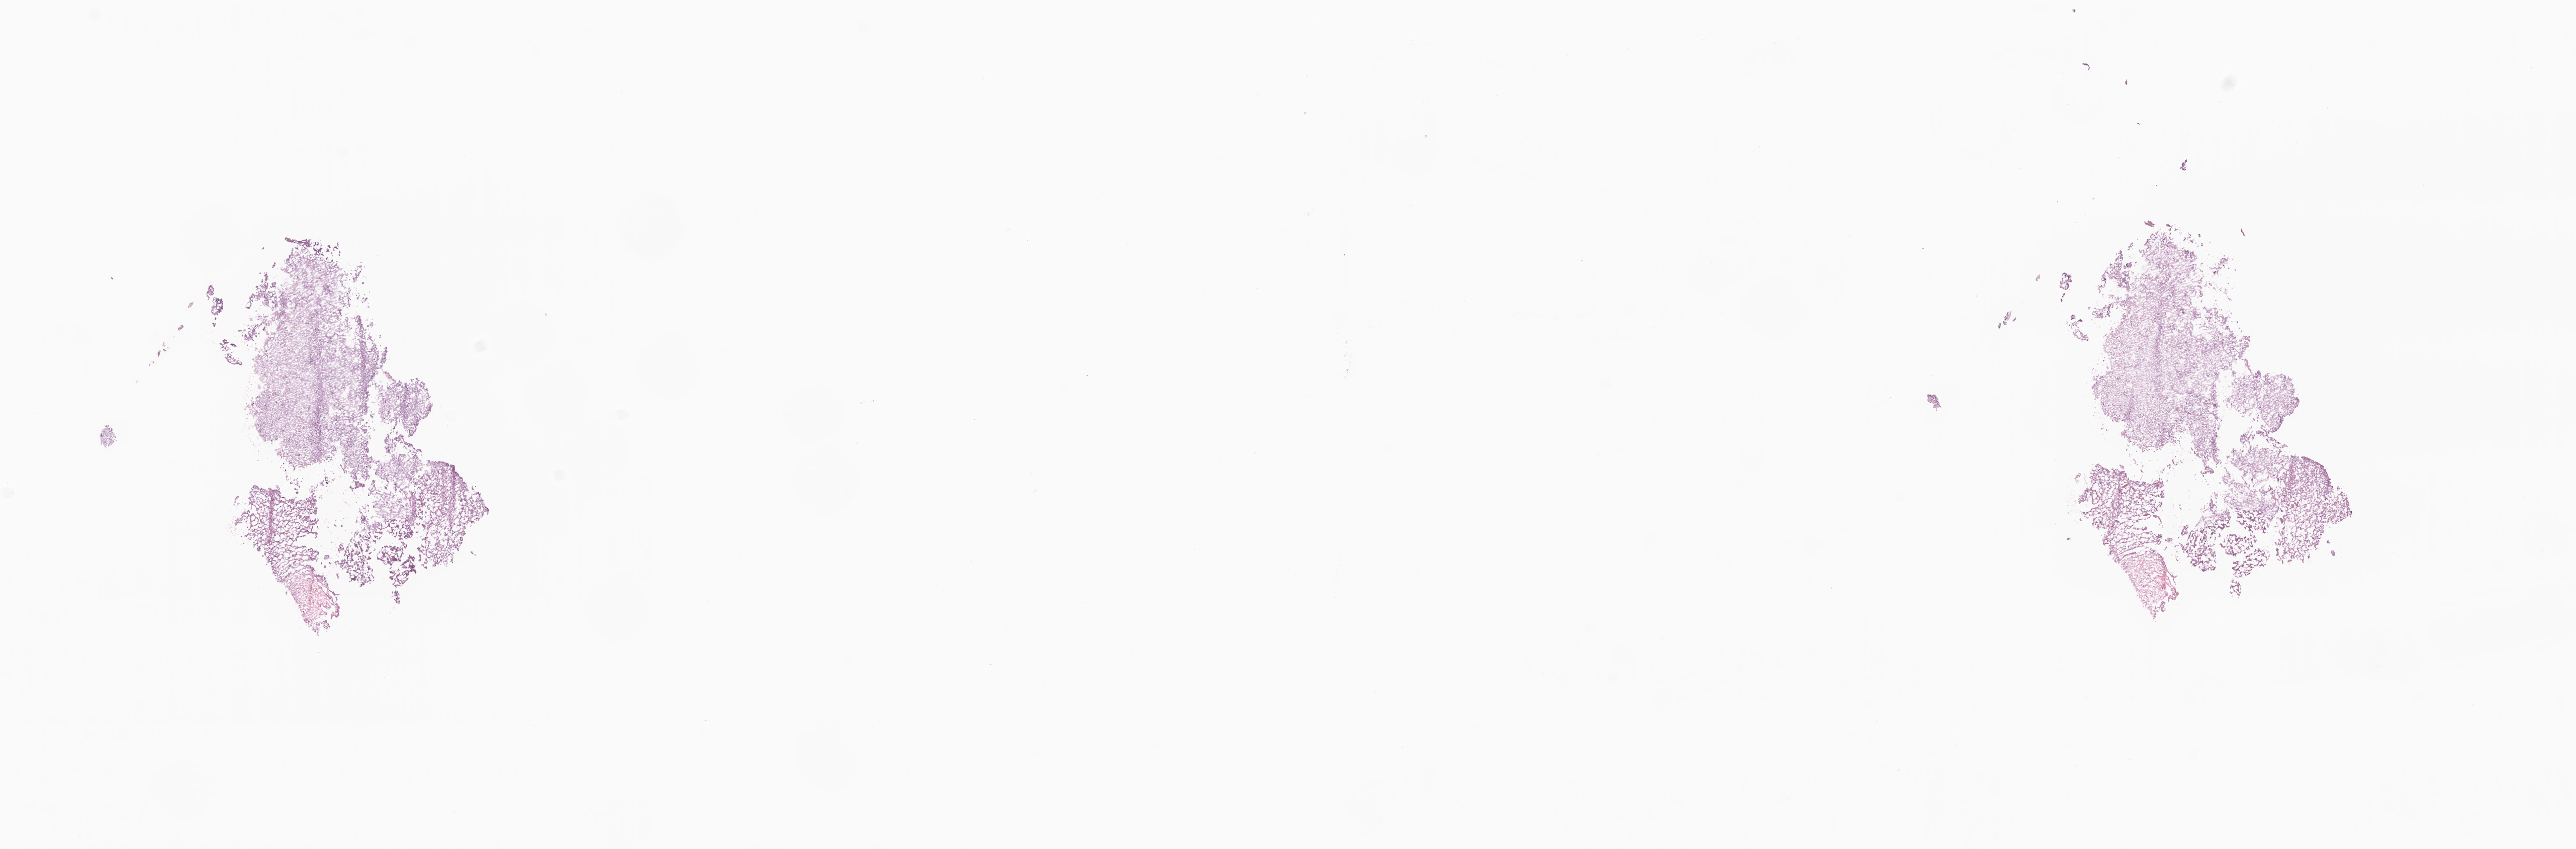
Digitized hematoxylin and eosin (H&E)-stained section of tumor tissue from the parietal lobe, shown as a low-resolution overview of the whole scanned area (about 21.6 x 7.1 mm). Cryosection (OCT / tissue freezing medium). Patient: male, age 73 months.
Recorded diagnosis: Giant cell glioblastoma.